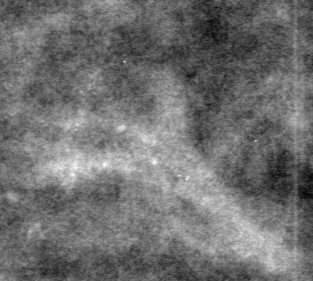
Crop from a digitized film mammogram around one marked abnormality; right breast; MLO view.
- Finding: calcifications, morphology pleomorphic, distribution clustered; BI-RADS assessment category 4; subtlety rating 2 on a 1 (subtle) to 5 (obvious) scale; pathology result (as recorded, not read from the image): benign.